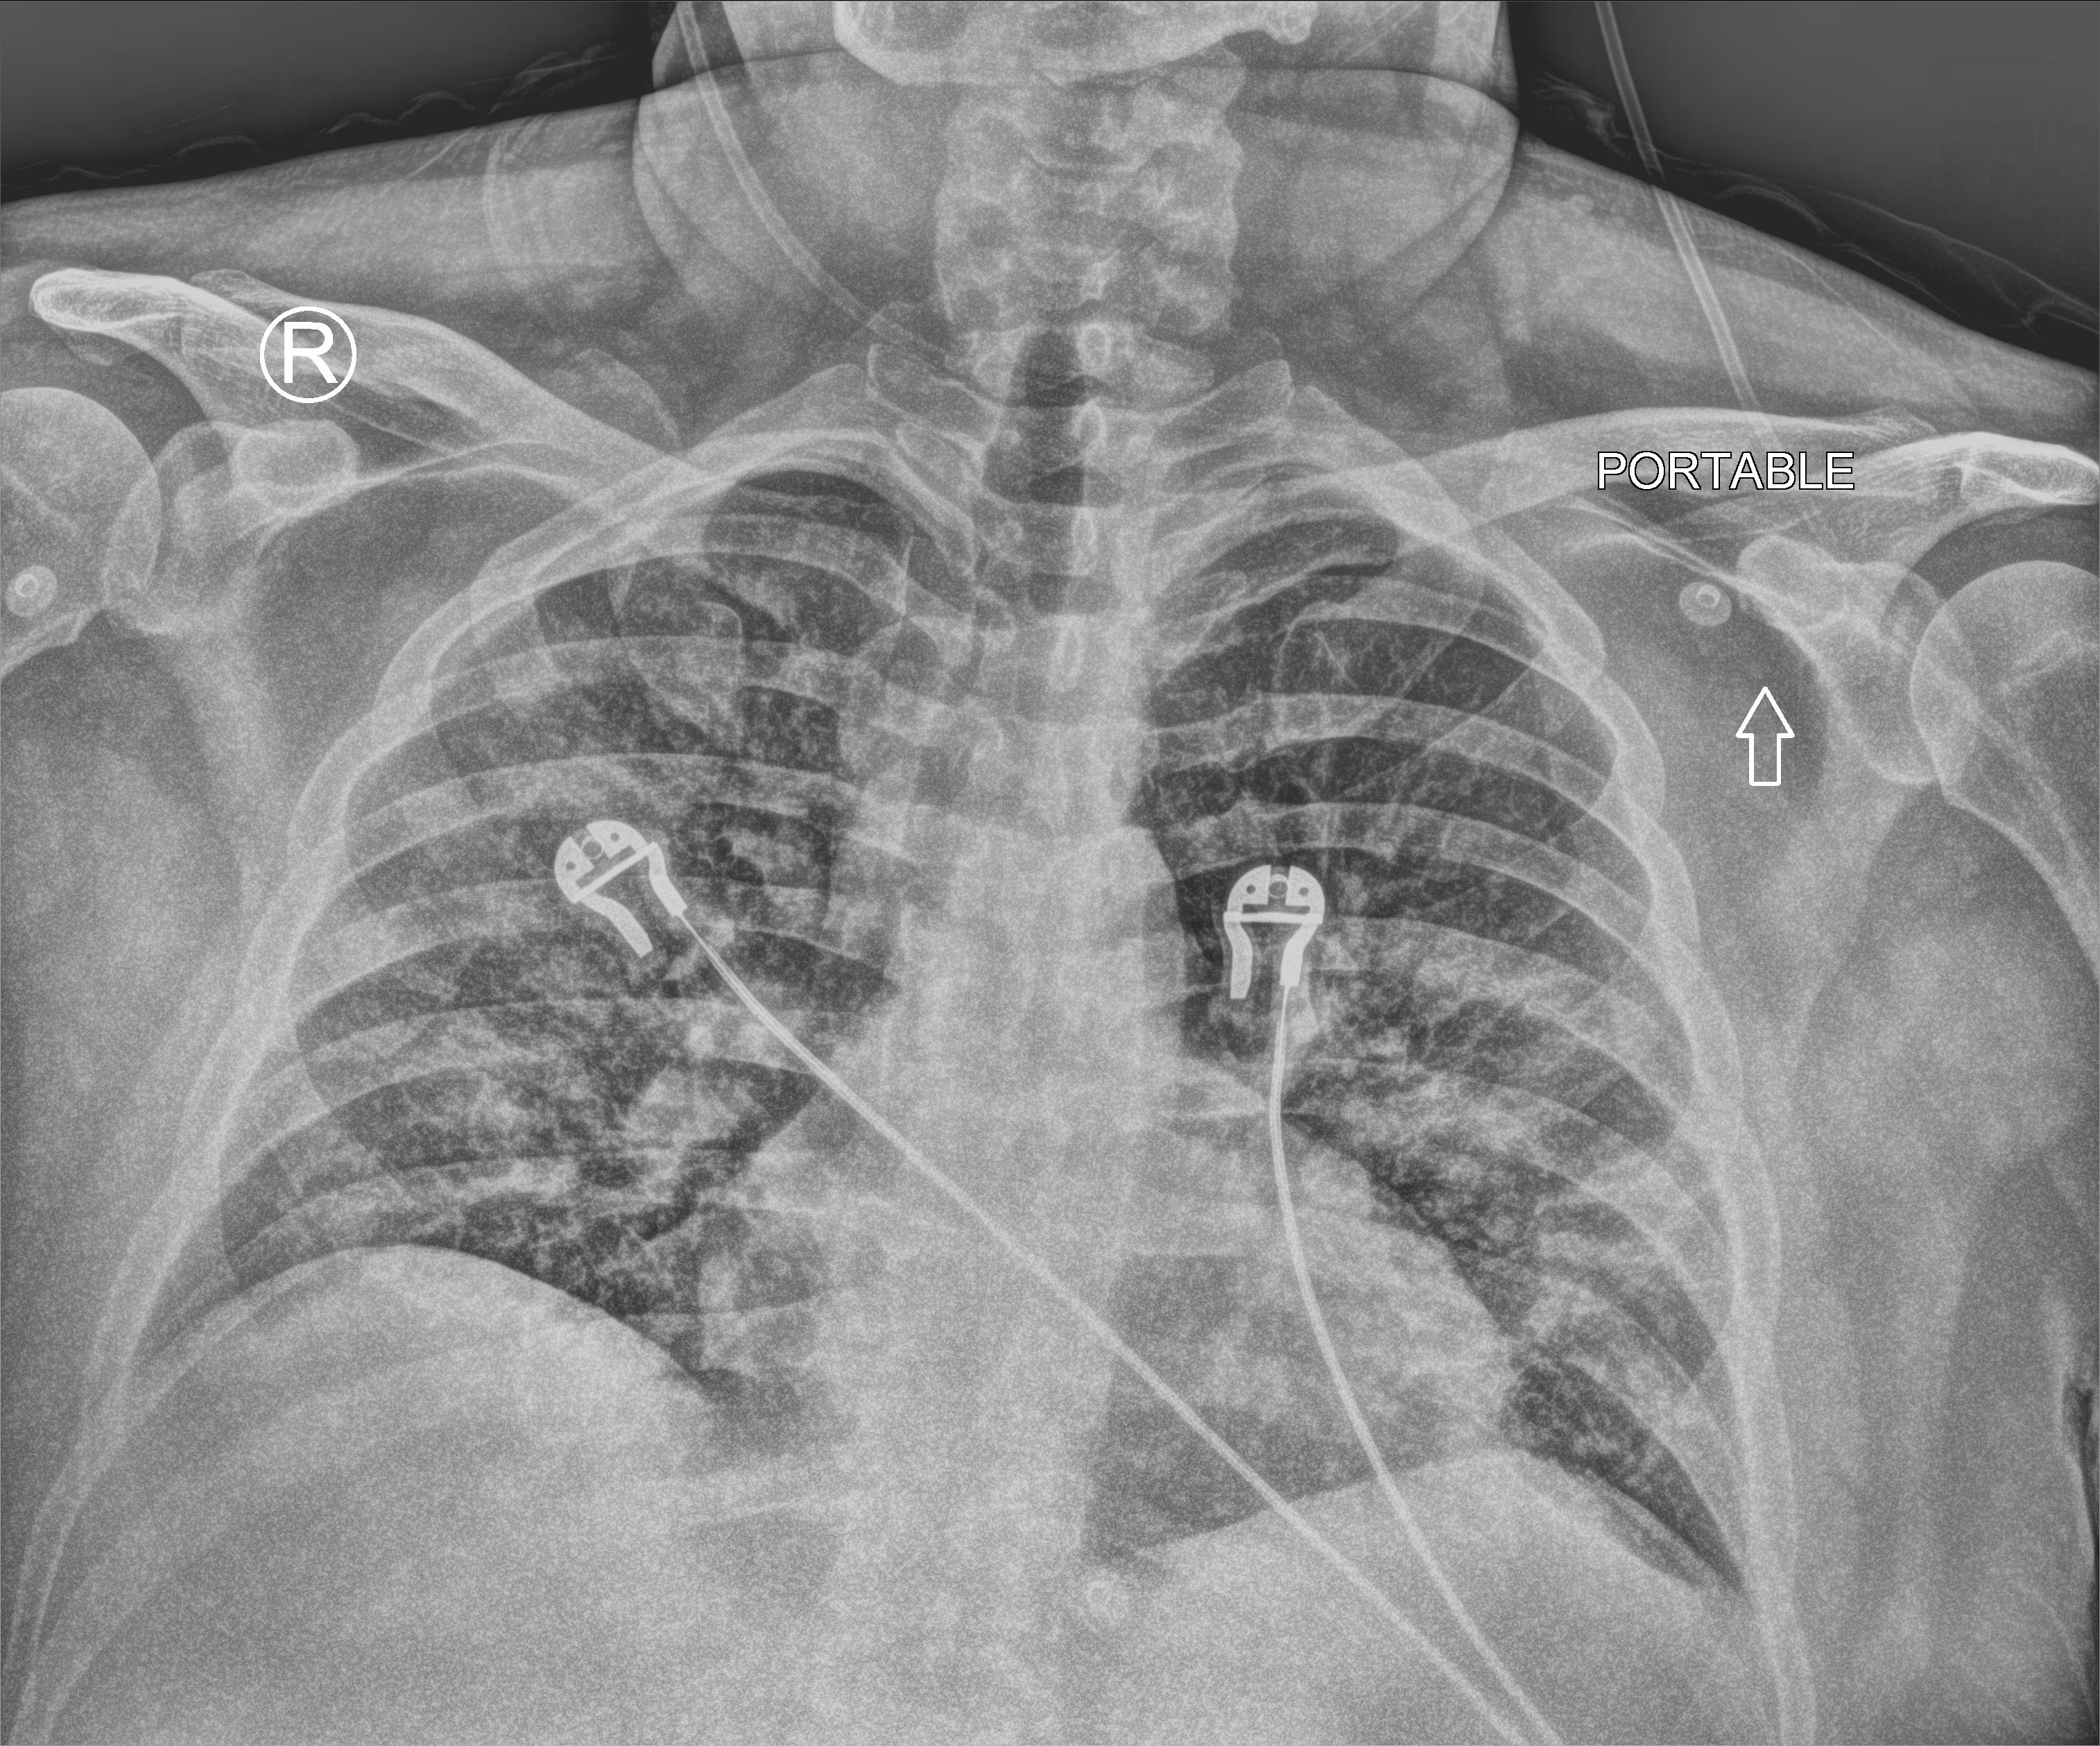
Bedside chest radiograph (computed radiography). Patient hospitalised with COVID-19; male, aged 18–59 years.
Hospital-stay facts (about this admission, not read from this image; timing relative to this image not recorded): length of hospital stay: 80 days; diabetes (admission record): no; admitted to intensive care during this hospital stay: yes.